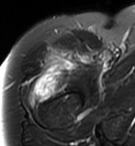
MRI of an extremity soft-tissue mass, one axial slice; slice 81 of 95 in the series (ordered by position); T2-weighted fat-saturated; MR volume resampled by the dataset authors to the PET/CT grid (not the native acquisition matrix); 135 × 146 image matrix, field of view 132 × 143 mm. Female patient. Case-level facts recorded for this patient, not image findings: histological type: pleiomorphic undifferentiated sarcoma; grade: high; site of the primary tumour: right quadricep.
Structures marked on this image (expert contour drawn on MRI and transferred to this co-registered scan by the dataset authors):
- gross tumour volume including surrounding oedema: bounding box (x1, y1, x2, y2) in pixels: (28, 47, 86, 105)